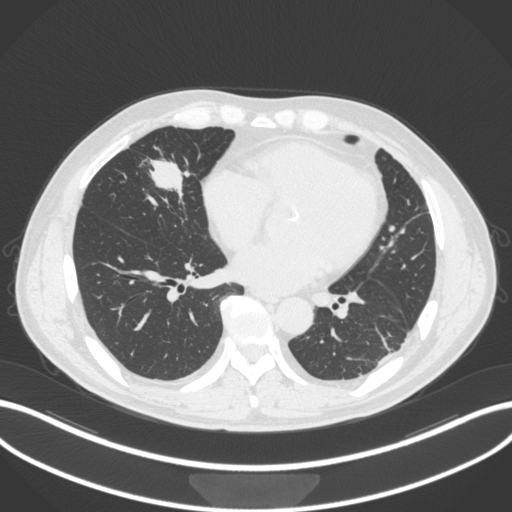
Chest CT, one axial slice; slice 110 of 399 in the series (ordered by position); reconstruction kernel B31f; lung window (W 1500 / L -600 HU); 1 mm slice thickness; 512 × 512 image matrix, field of view 400 × 400 mm. Patient: male, 59 years. From the clinical record (not read from this slice): clinical TNM (as recorded): T2a N1 M0.
Structures marked on this image (bounding box drawn by a radiologist):
- lung tumour (recorded histology: adenocarcinoma): box from (x=139, y=153) to (x=195, y=203) px